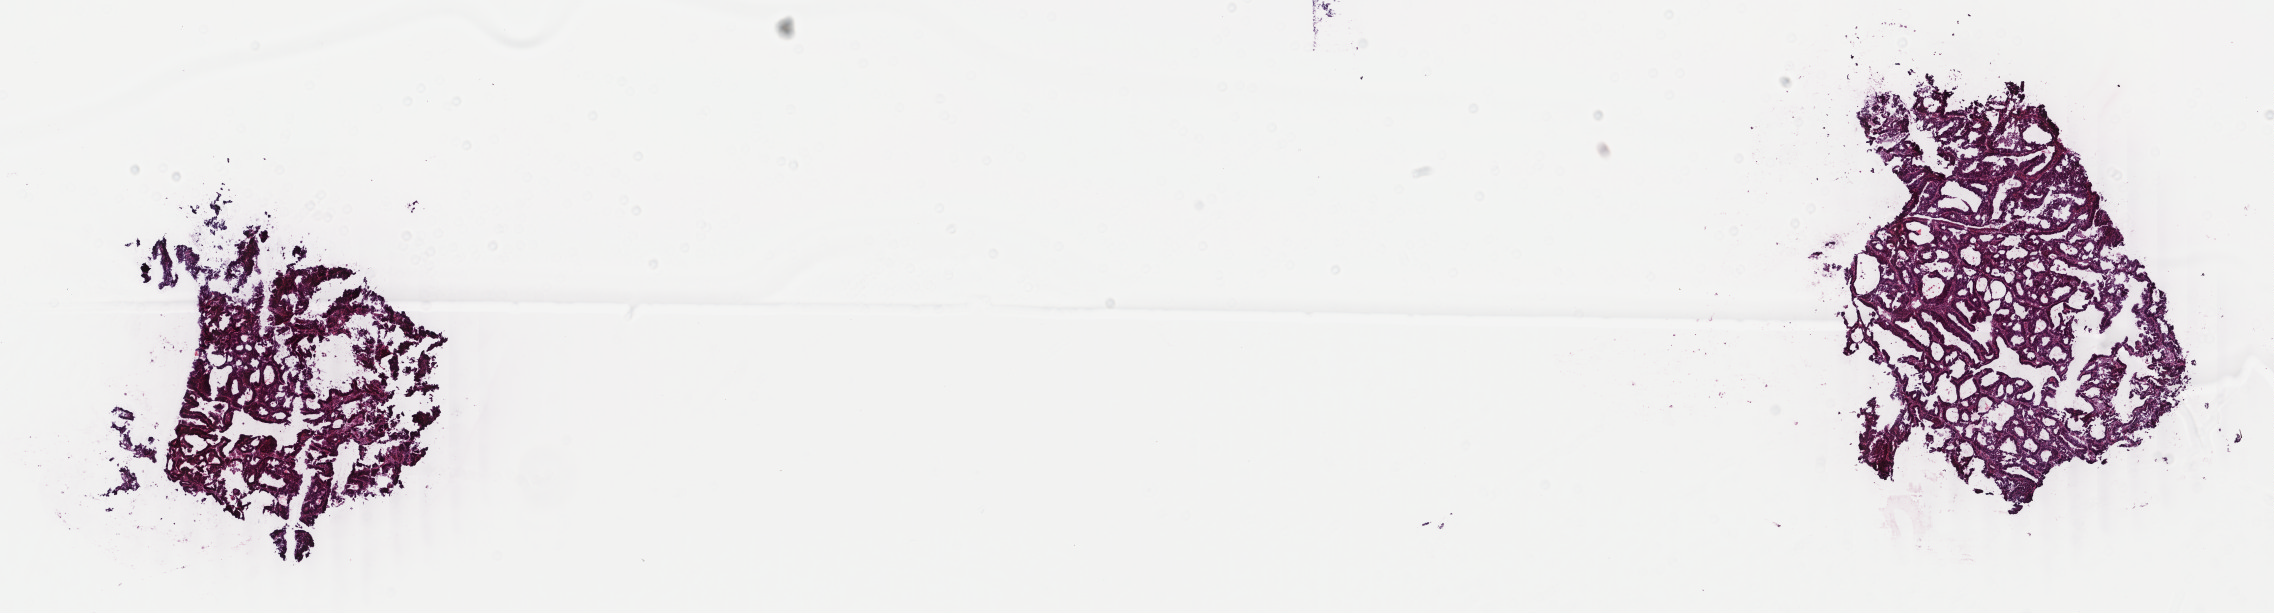
H&E-stained whole-slide image — shown as a low-resolution overview of the whole scanned area (about 18.1 x 4.9 mm); frozen section from the top of the tissue portion; sample: primary tumour, uterus. Patient: female, age at initial diagnosis 61 years. Histologic grade: G1 (well differentiated). Pathologist review of this section (percent, as recorded): tumour cells 70%, tumour nuclei 70%, normal cells 10%, stromal cells 15%, necrosis 5%. Infiltration values recorded for this section: lymphocyte infiltration 40%, monocyte infiltration 20%, neutrophil infiltration 20%.
FIGO stage: IA. Diagnosis: Endometrioid adenocarcinoma, NOS (endometrium).